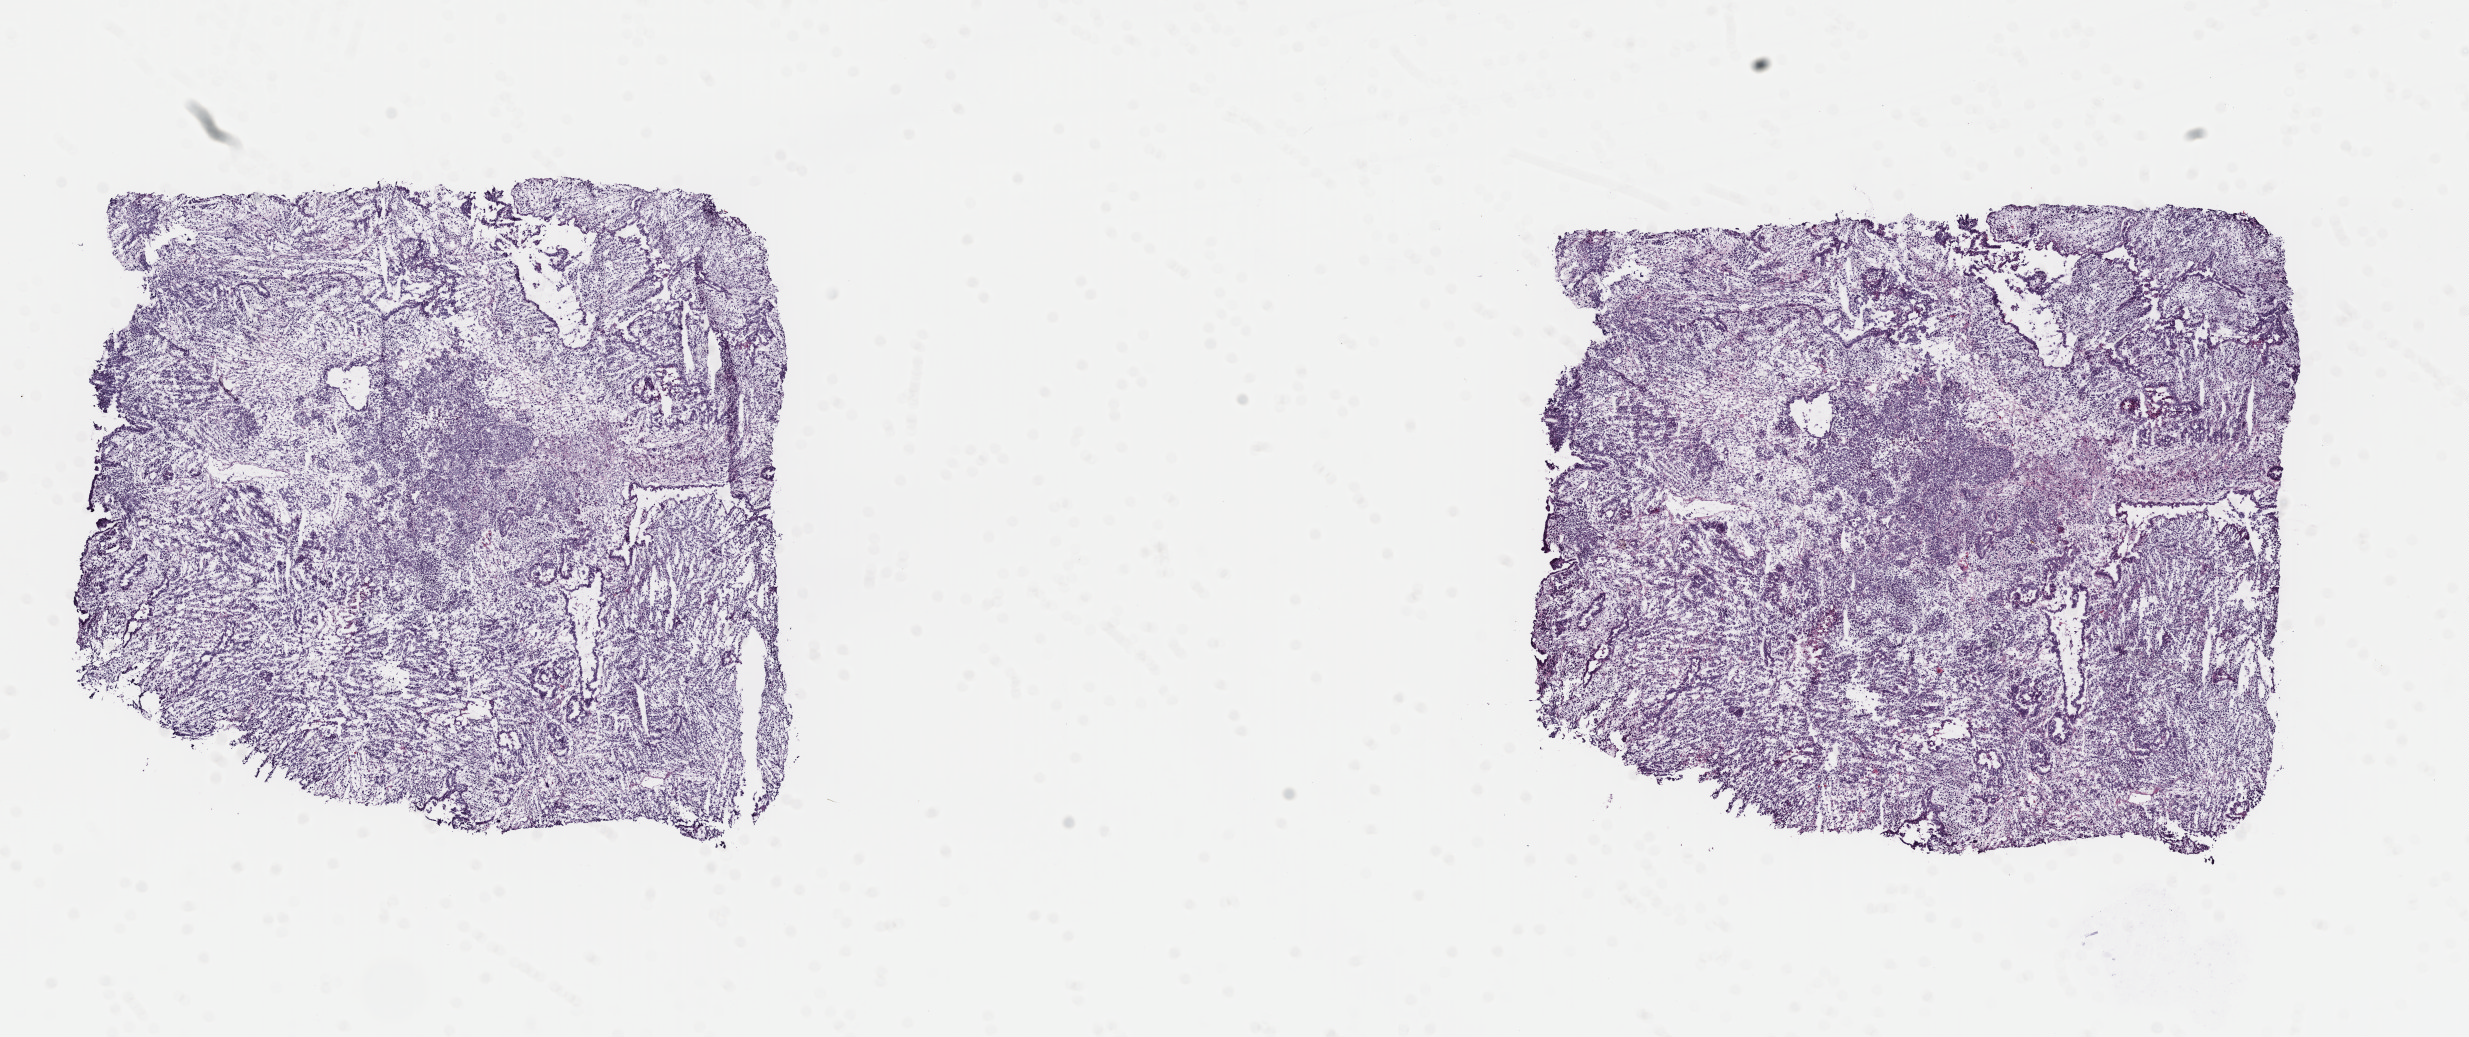
Hematoxylin and eosin (H&E) stained whole-slide image, whole scanned area (about 19.5 x 8.2 mm, acquisition: 40x scan) shown as a low-resolution overview. Frozen section from the top of the tissue portion. Primary tumour sample from the uterus. Patient: female, age at initial diagnosis 61 years. Pathologist review of this section (percent, as recorded): tumour cells 80%, tumour nuclei 80%, normal cells 0%, stromal cells 20%, necrosis 0%. Inflammatory infiltration, as recorded: lymphocyte infiltration 40%, monocyte infiltration 20%, neutrophil infiltration 20%.
Diagnosis: Mullerian mixed tumor. FIGO stage: IV.